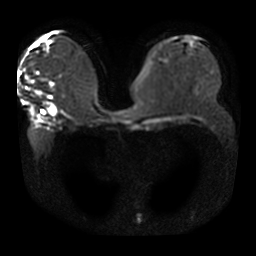
Breast MRI, one axial slice. Position 20 of 42 along the scan axis. Diffusion-weighted series; image 2 of 4 stored at this slice position (different b-values; order by instance number). 3 T. 5 mm slice thickness. 256 × 256 image matrix, field of view 360 × 360 mm. Female patient.
Outlined on this slice (outlined manually by an expert reader):
- tumour on diffusion-weighted imaging: bounding box (x1, y1, x2, y2) in pixels: (34, 91, 56, 115)